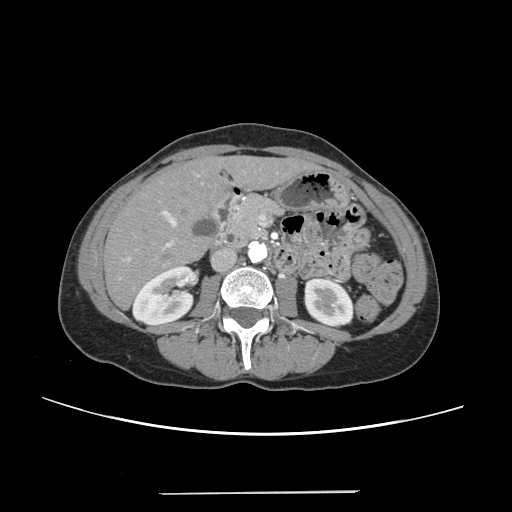
Contrast-enhanced abdominal CT, one axial slice; slice 100 of 240 in the series (ordered by position); intravenous contrast given; soft-tissue window (W 400 / L 40 HU); 1.25 mm slice thickness; 512 × 512 image matrix, field of view 371 × 371 mm. Female patient, age 60 years. From the clinical record (not read from this slice): diagnosis: colorectal cancer liver metastases, imaged before liver resection; multiple liver metastases: no; largest metastasis: 1.5 cm; chemotherapy before resection: yes.
Outlined on this slice (expert manual segmentation):
- liver: bounding box [x1, y1, x2, y2] px = [105, 158, 308, 308]
- planned liver remnant (the part of the liver to remain after resection): [105, 159, 308, 308]
- portal vein (with intrahepatic branches): [122, 174, 199, 262]